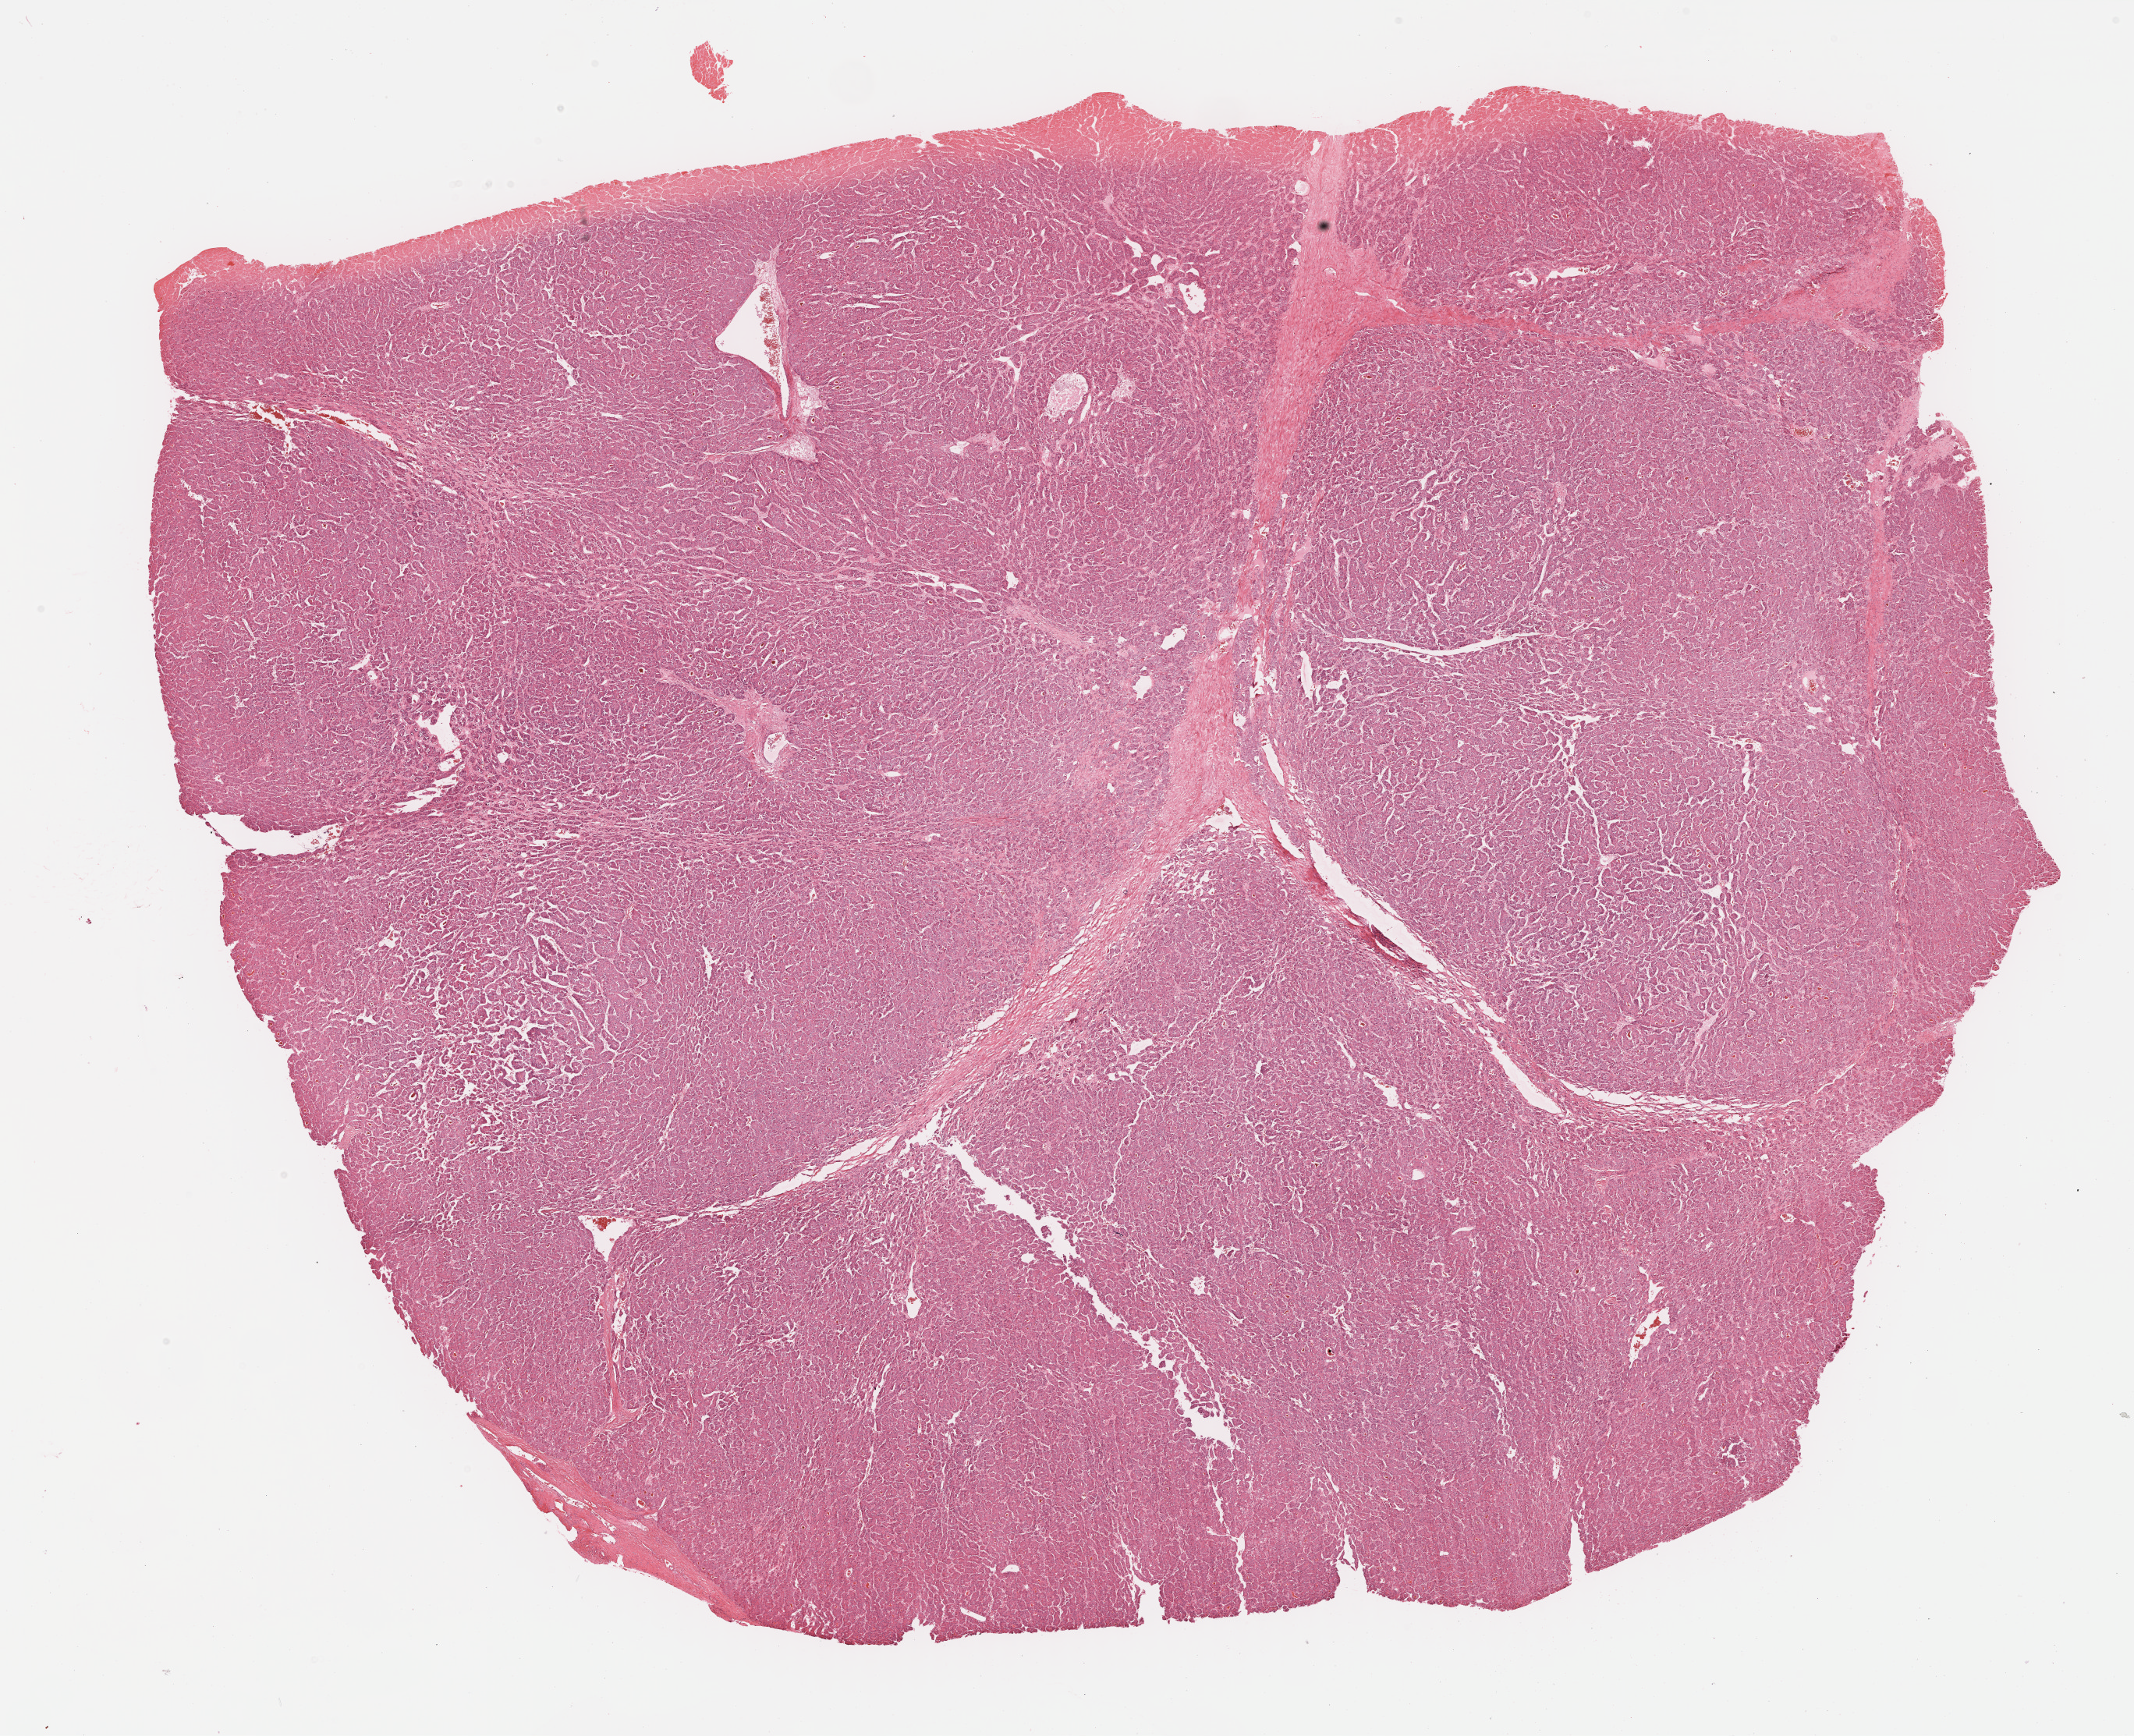
Digitized H&E tissue section (whole slide), whole scanned area (about 22.1 x 18.0 mm) shown as a low-resolution overview; formalin-fixed paraffin-embedded (FFPE) diagnostic section; primary tumour sample from the liver. Patient: male, age at initial diagnosis 45 years. Histologic grade: G2 (moderately differentiated).
Diagnosis: Hepatocellular carcinoma, NOS. AJCC pathologic stage: I (5th edition).